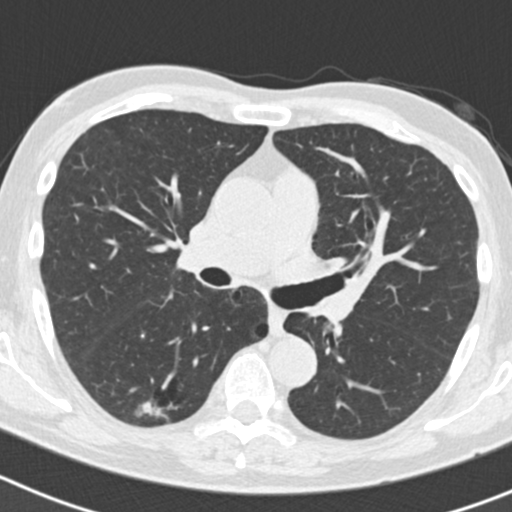
Chest CT (low-dose screening protocol), one axial image; second annual screen; lung window (W 1500 / L -600 HU); 2 mm slice thickness; 120 kVp; slice 74 of 186 in the series; 512 × 512 image matrix, field of view 300 × 300 mm. Male participant, aged 70 years at enrolment. Current smoker at enrolment.
Expert reader's lesion annotation, bounding box (x1, y1, x2, y2) in pixels: (133, 377, 196, 433). The screening reader recorded 5 non-calcified nodules or masses ≥4 mm on this exam (right lower lobe, right lower lobe, right upper lobe, right upper lobe, left upper lobe); which of them this box marks is not recorded. Participant outcome: lung cancer diagnosed 622 days after this screen (after the third annual screen) — bronchiolo-alveolar adenocarcinoma, NOS, right lower lobe, poorly differentiated (G3), stage IB (AJCC 6th edition), 30 mm at pathology.